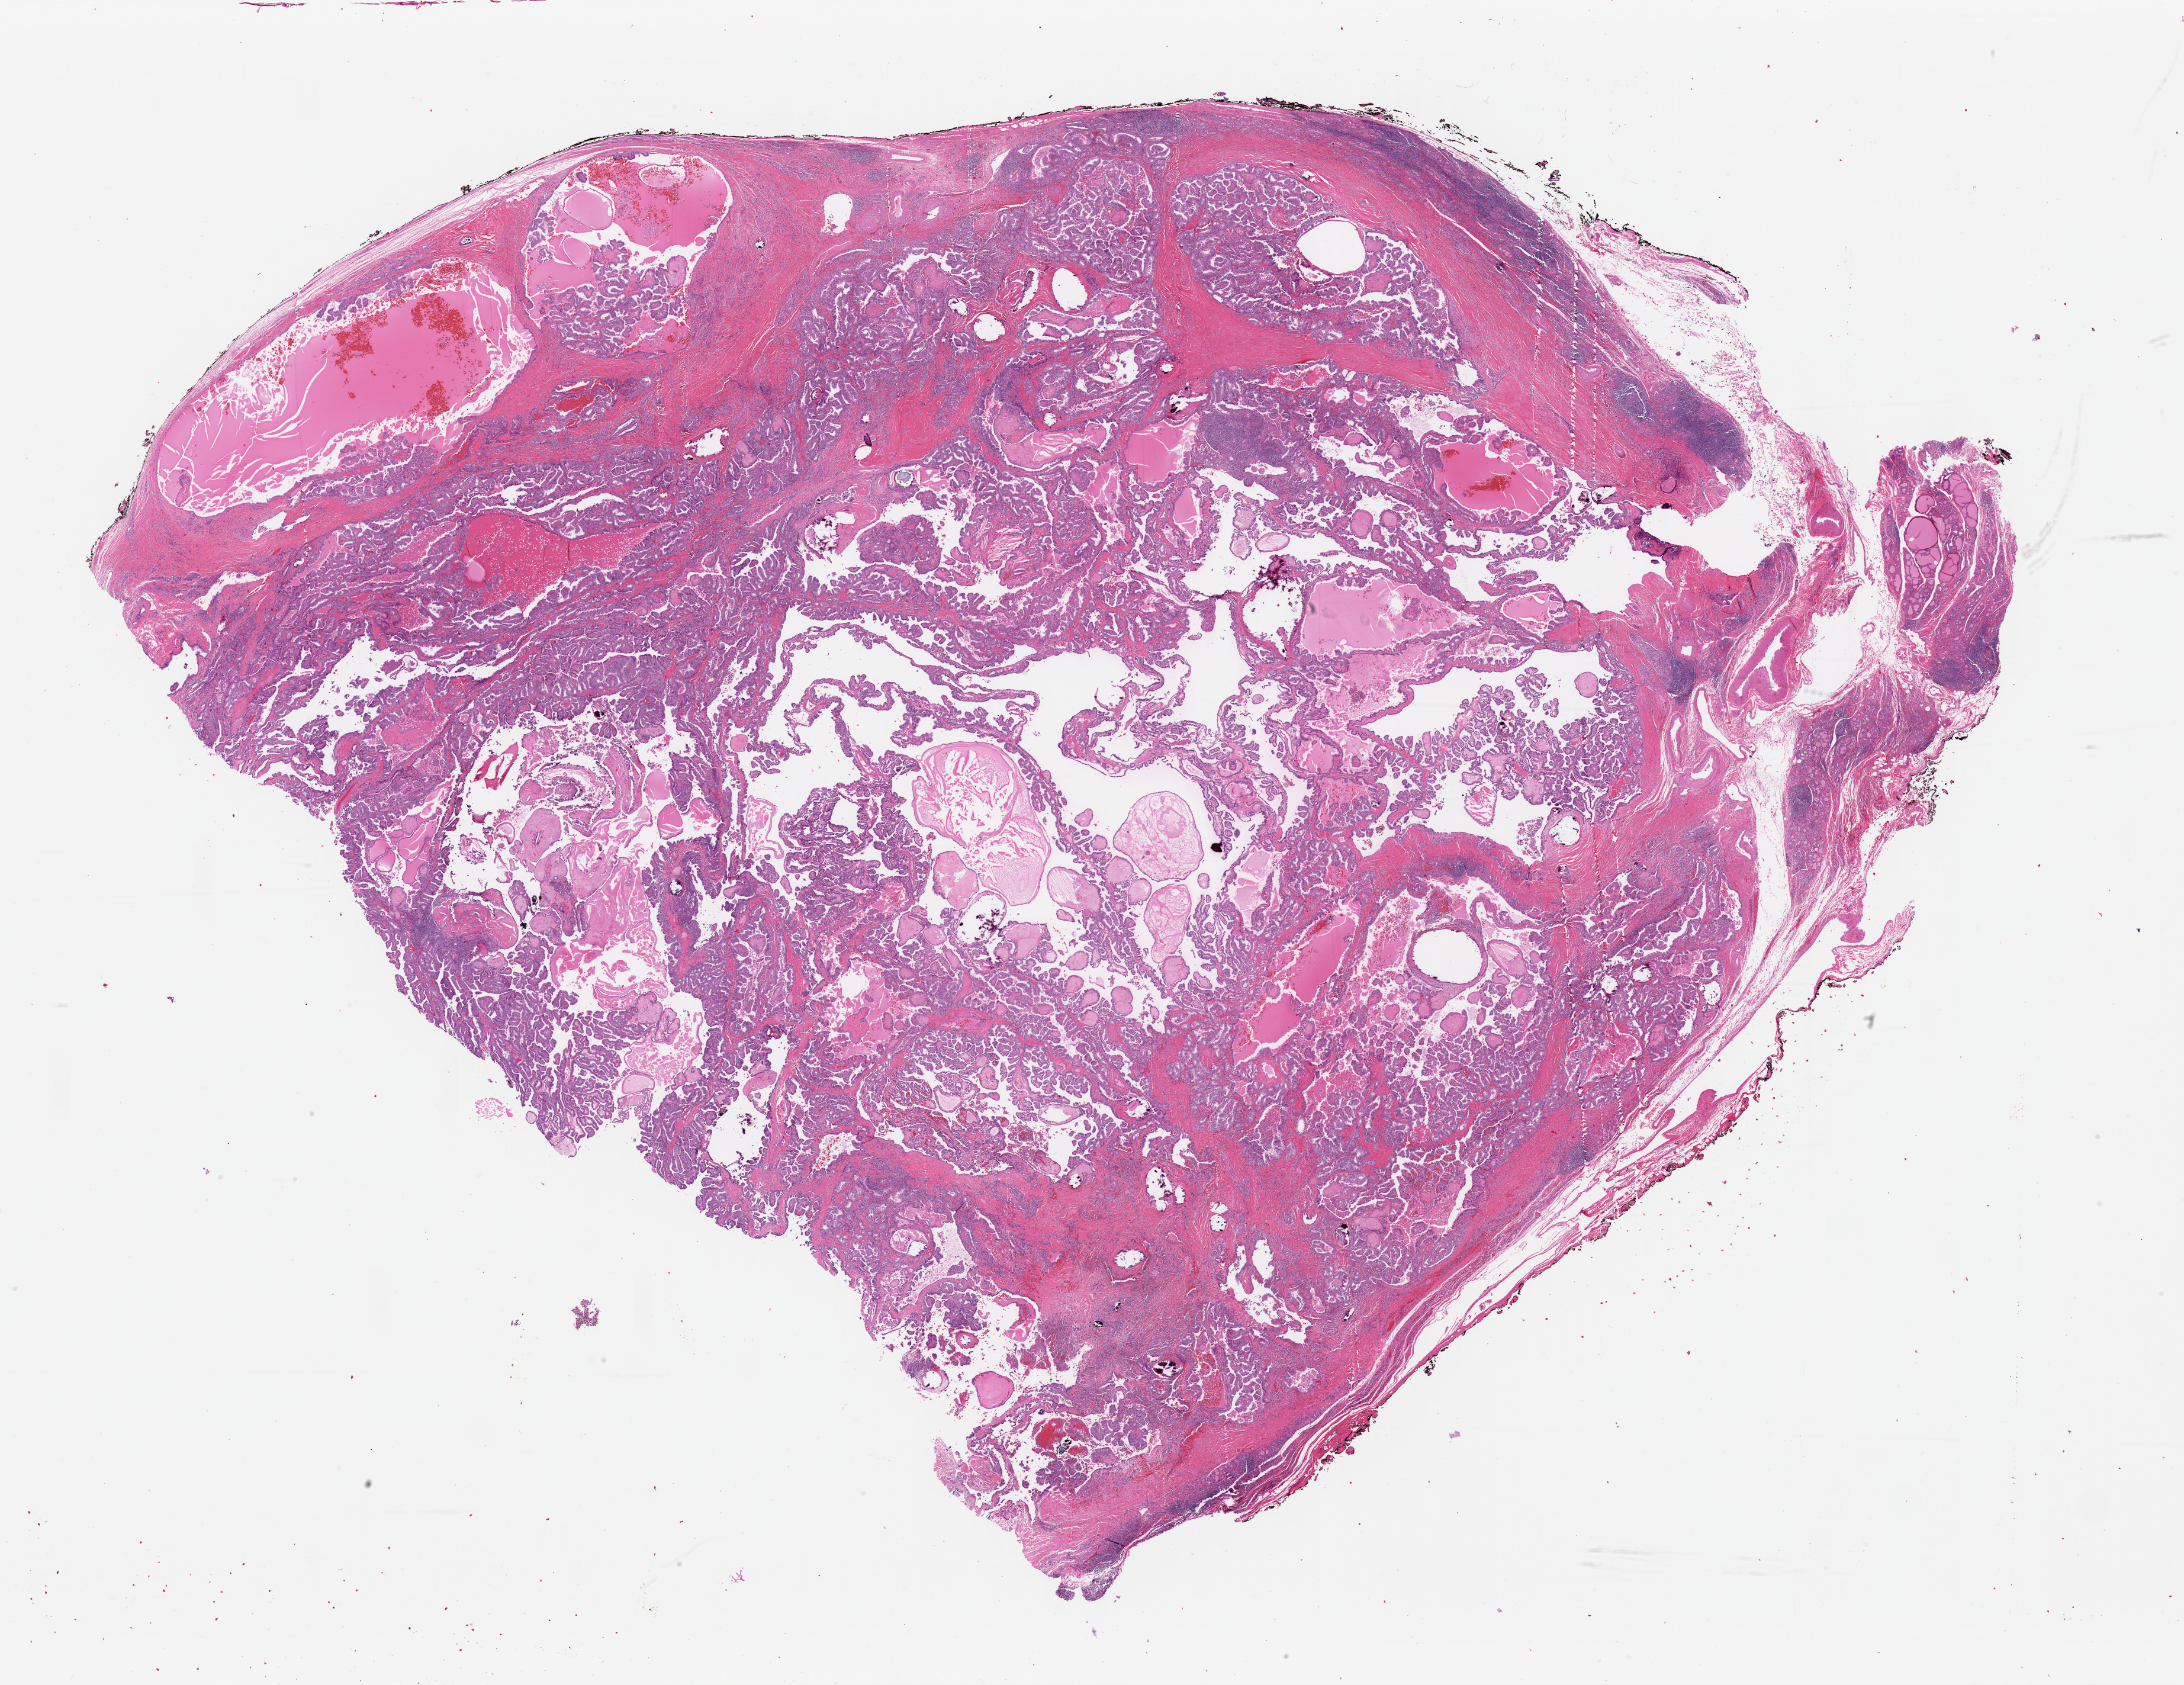
H&E-stained whole-slide image, whole scanned area (about 29.1 x 22.5 mm, slide scanned at 40x) shown as a low-resolution overview, formalin-fixed paraffin-embedded (FFPE) diagnostic section, thyroid, primary tumour sample. Male, age 34 years at initial diagnosis.
* AJCC pathologic stage: I (6th edition)
* laterality: left
* pathologic diagnosis: Papillary adenocarcinoma, NOS (thyroid gland)